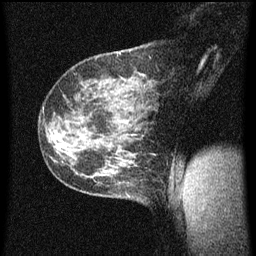
Breast MRI (dynamic contrast-enhanced), one sagittal slice. Position 40 of 60 along the scan axis. Dynamic contrast-enhanced series, image 2 of 3 at this slice position (ordered by acquisition). 1.5 T. TE 4.2 ms, TR 8 ms. 2 mm slice thickness. 256 × 256 image matrix. Patient: female, 35 years.
Outlined on this slice (semi-automatic segmentation, software-assisted and operator-edited):
- analysis volume of interest (the breast-tissue region the enhancement analysis was run in; not a lesion): bounding box <106,182,149,205> (left, top, right, bottom; pixels)
- tumour enhancement mask (voxels above the 70 % enhancement threshold inside the analysis volume of interest): <128,184,133,197>